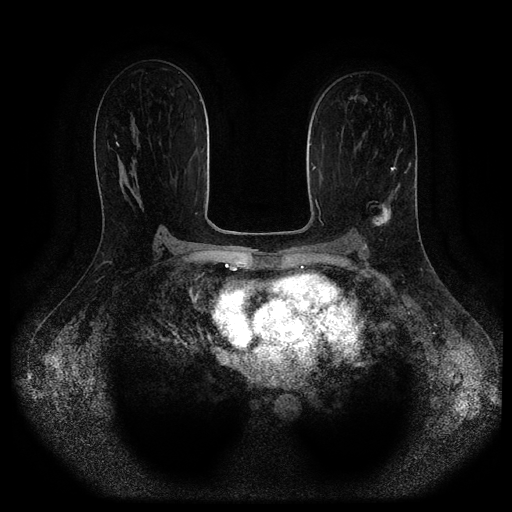
Breast MRI (dynamic contrast-enhanced, multi-phase), one axial slice; position 61 of 116 along the scan axis; dynamic contrast-enhanced series, time point 2 of 5 at this slice position (early post-contrast); 1.5 T; TE 2.6 ms, TR 5.3 ms; 2 mm slice thickness; 512 × 512 image matrix, field of view 370 × 370 mm. Patient: female, 45 years.
Outlined on this slice (semi-automatically segmented with operator editing):
- breast lesion (labelled 'tumour' in the annotation; benign lesions carry a separate 'benign' label): bounding box (x1, y1, x2, y2) in pixels: (371, 203, 393, 226)